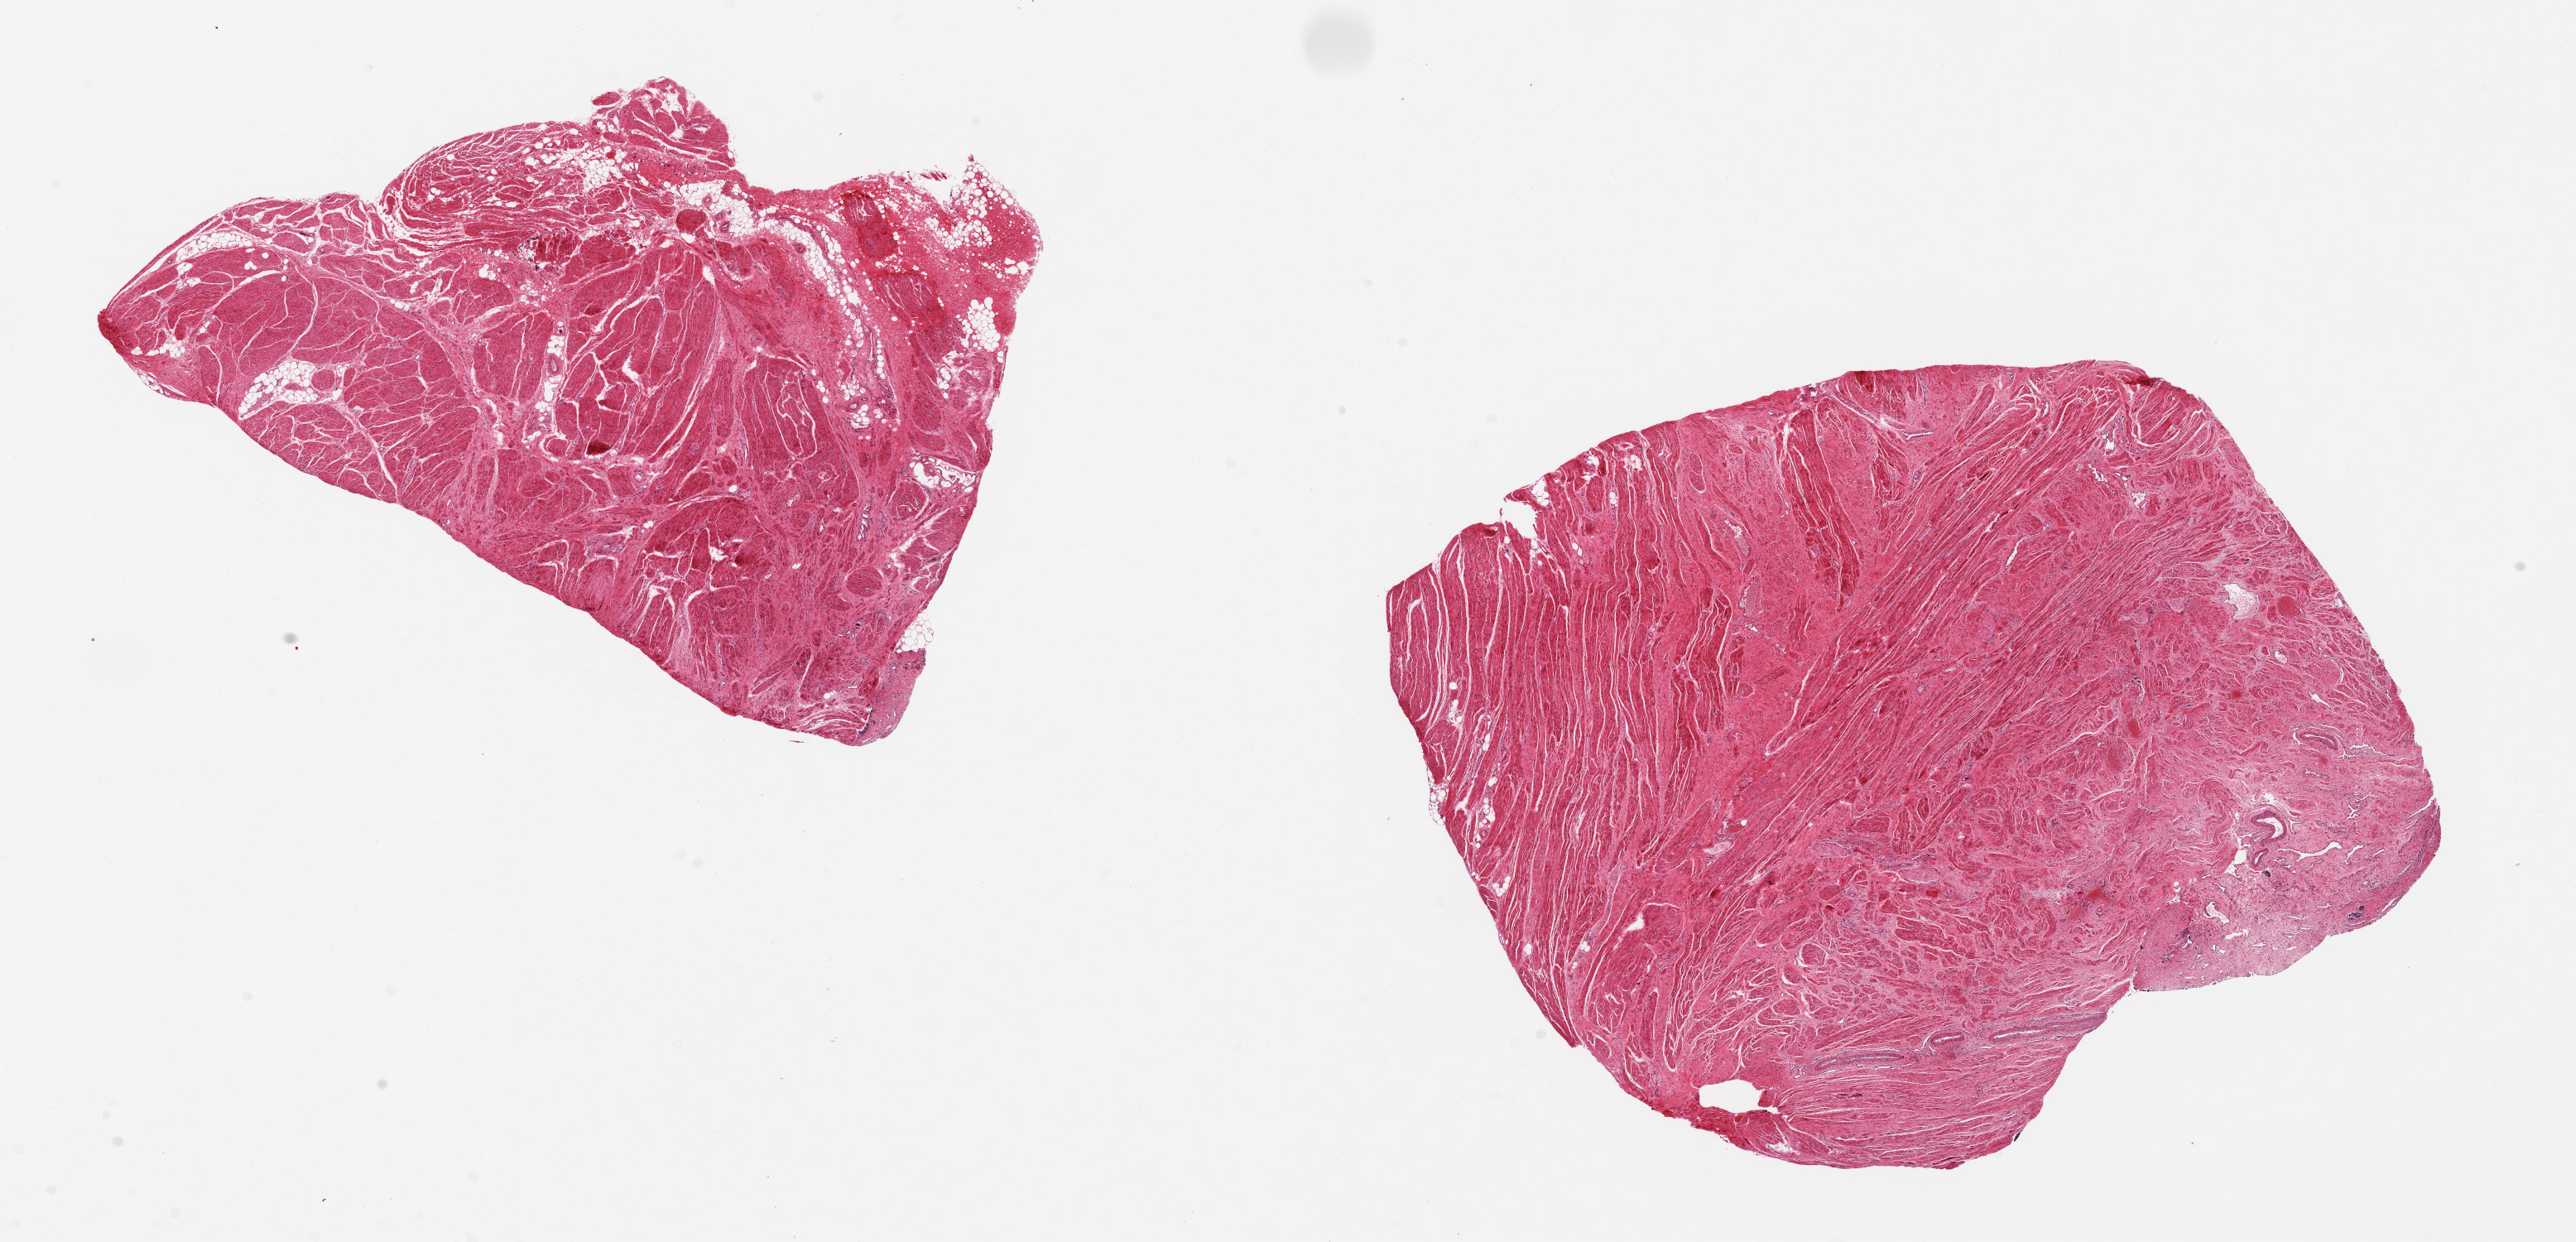
H&E whole-slide image — a low-resolution overview of the entire scanned area, about 24.6 x 11.9 mm (from a 20x scan). PAXgene-fixed paraffin-embedded (PFPE) section. Sampled site (target tissue): prostate. Donor tissue sample. Male donor.
* reviewer comment on this tissue sample: 2 pieces 8x7 & 8x5 mm; fibromuscular content, no glands